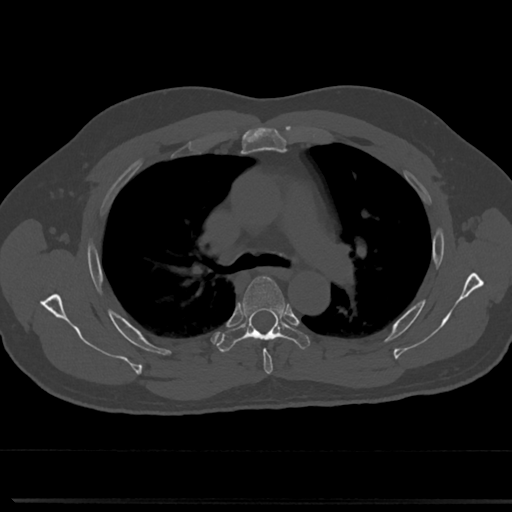
CT including the spine, one axial slice; slice 512 of 817 in the series (ordered by position); reconstruction kernel Br40s/3; bone window (W 1800 / L 400 HU); 0.5 mm slice thickness; 512 × 512 image matrix, field of view 355 × 355 mm. Male patient, age 61 years. From the clinical record (not read from this slice): primary cancer: prostate.
Outlined on this slice (semi-automatically segmented with operator editing):
- T4 vertebra: bounding box [x1, y1, x2, y2] px = [242, 285, 283, 373]
- T5 vertebra: [219, 276, 310, 352]